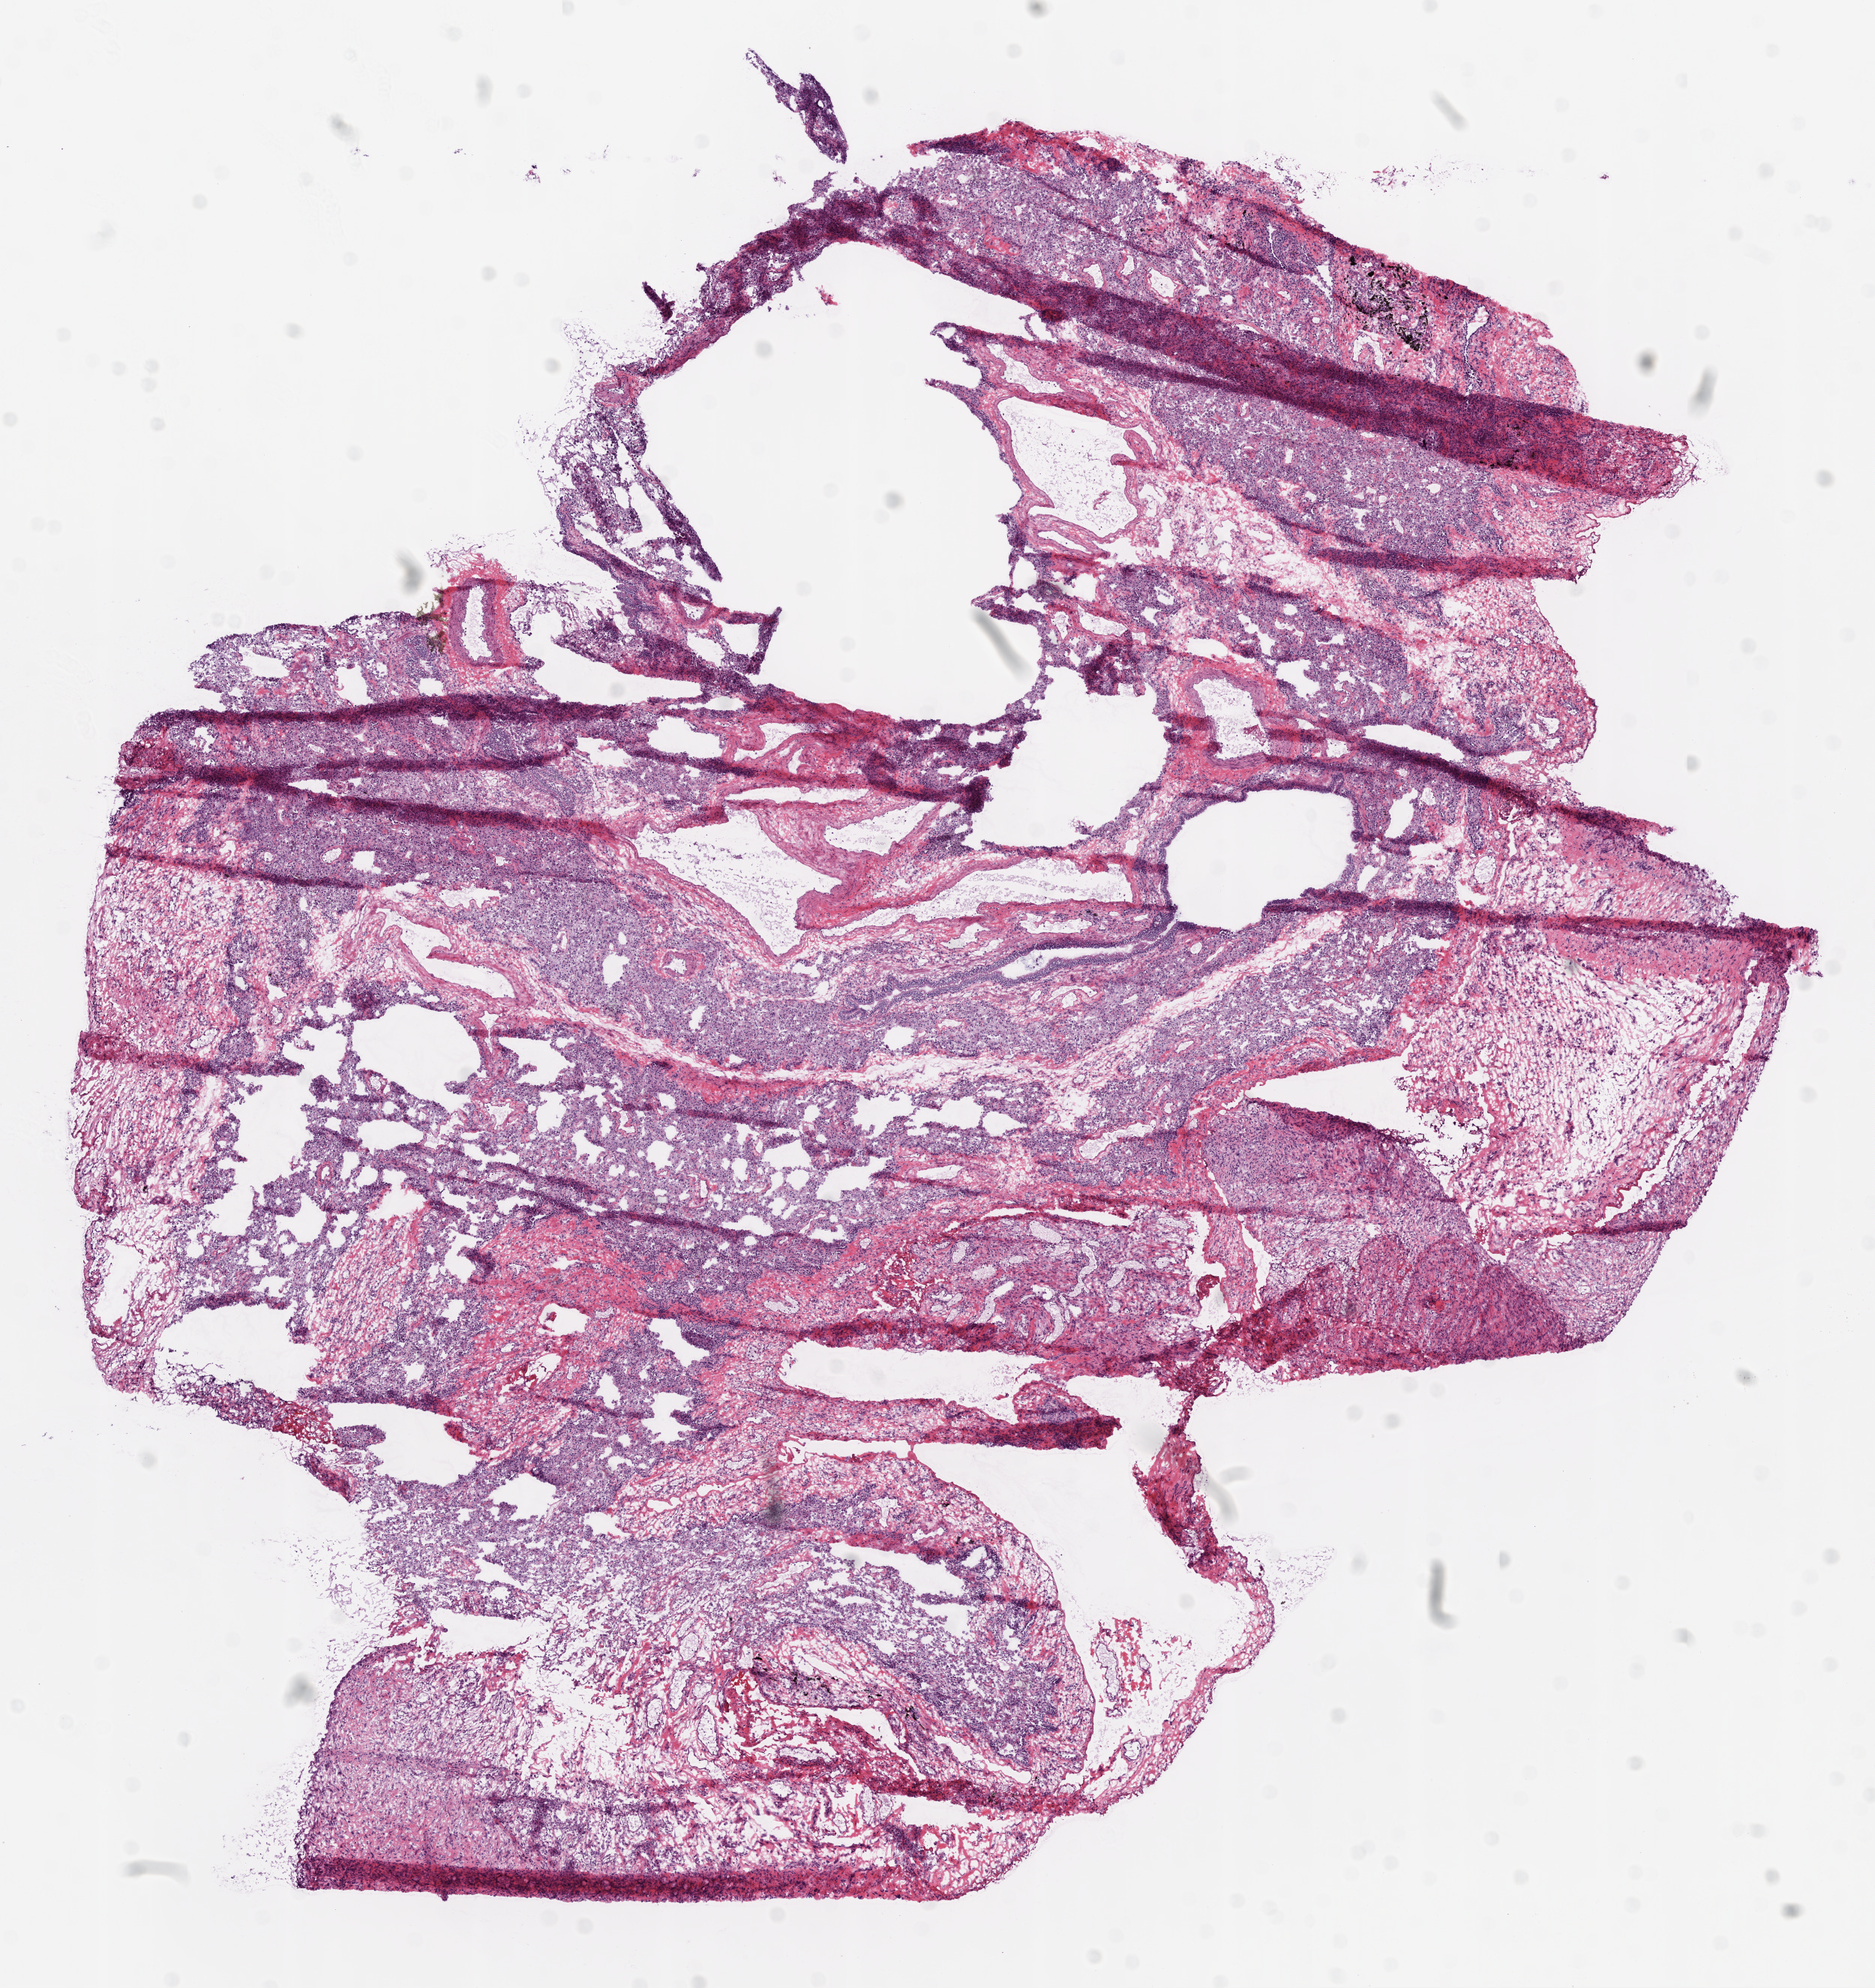
H&E-stained whole-slide image, a low-resolution overview of the entire scanned area, about 10.0 x 10.6 mm, frozen section from the top of the tissue portion, lung, solid tissue normal (non-tumour tissue) sample. Patient: male, age at initial diagnosis 57 years.
This section: solid tissue normal (non-tumour) sample from the same patient. Patient diagnosis: Squamous cell carcinoma, NOS (lower lobe, lung).